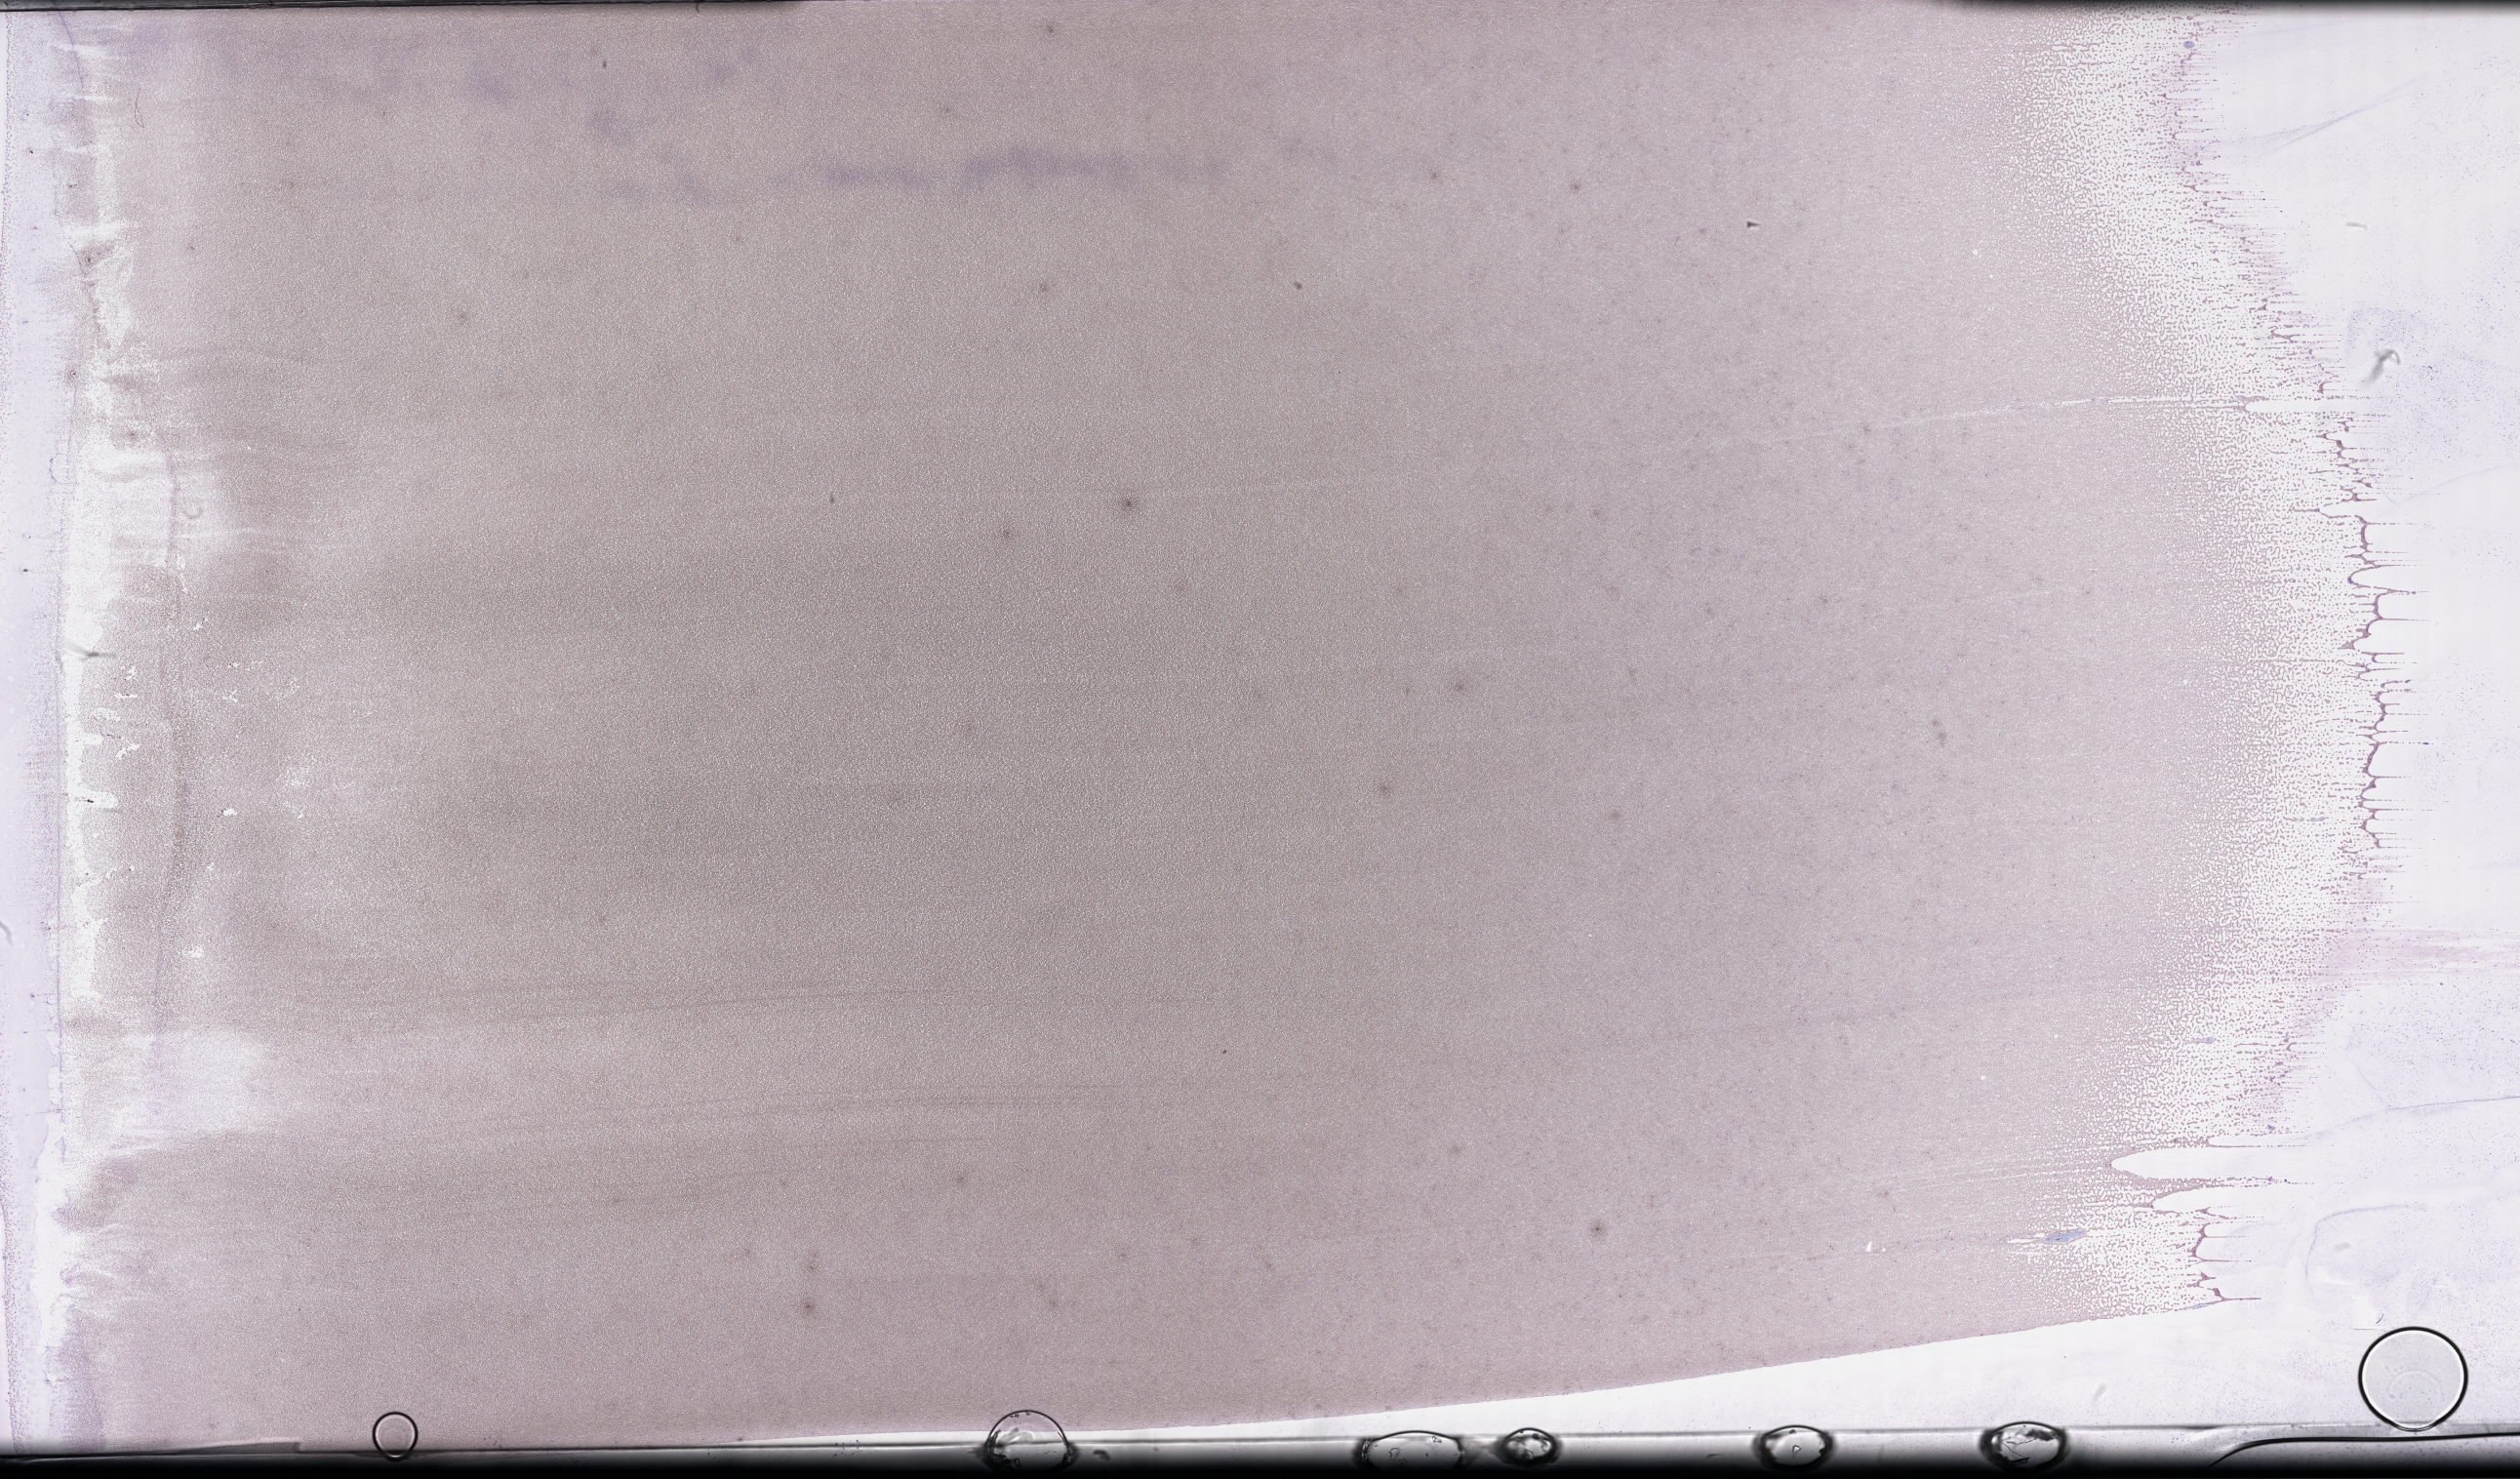
Wright-Giemsa-stained whole blood smear, whole-slide image — low-resolution overview of the scanned area, about 41.7 x 24.5 mm. Specimen time point: collected on treatment. Patient sex: male.
From a patient with: Plasma Cell Myeloma.